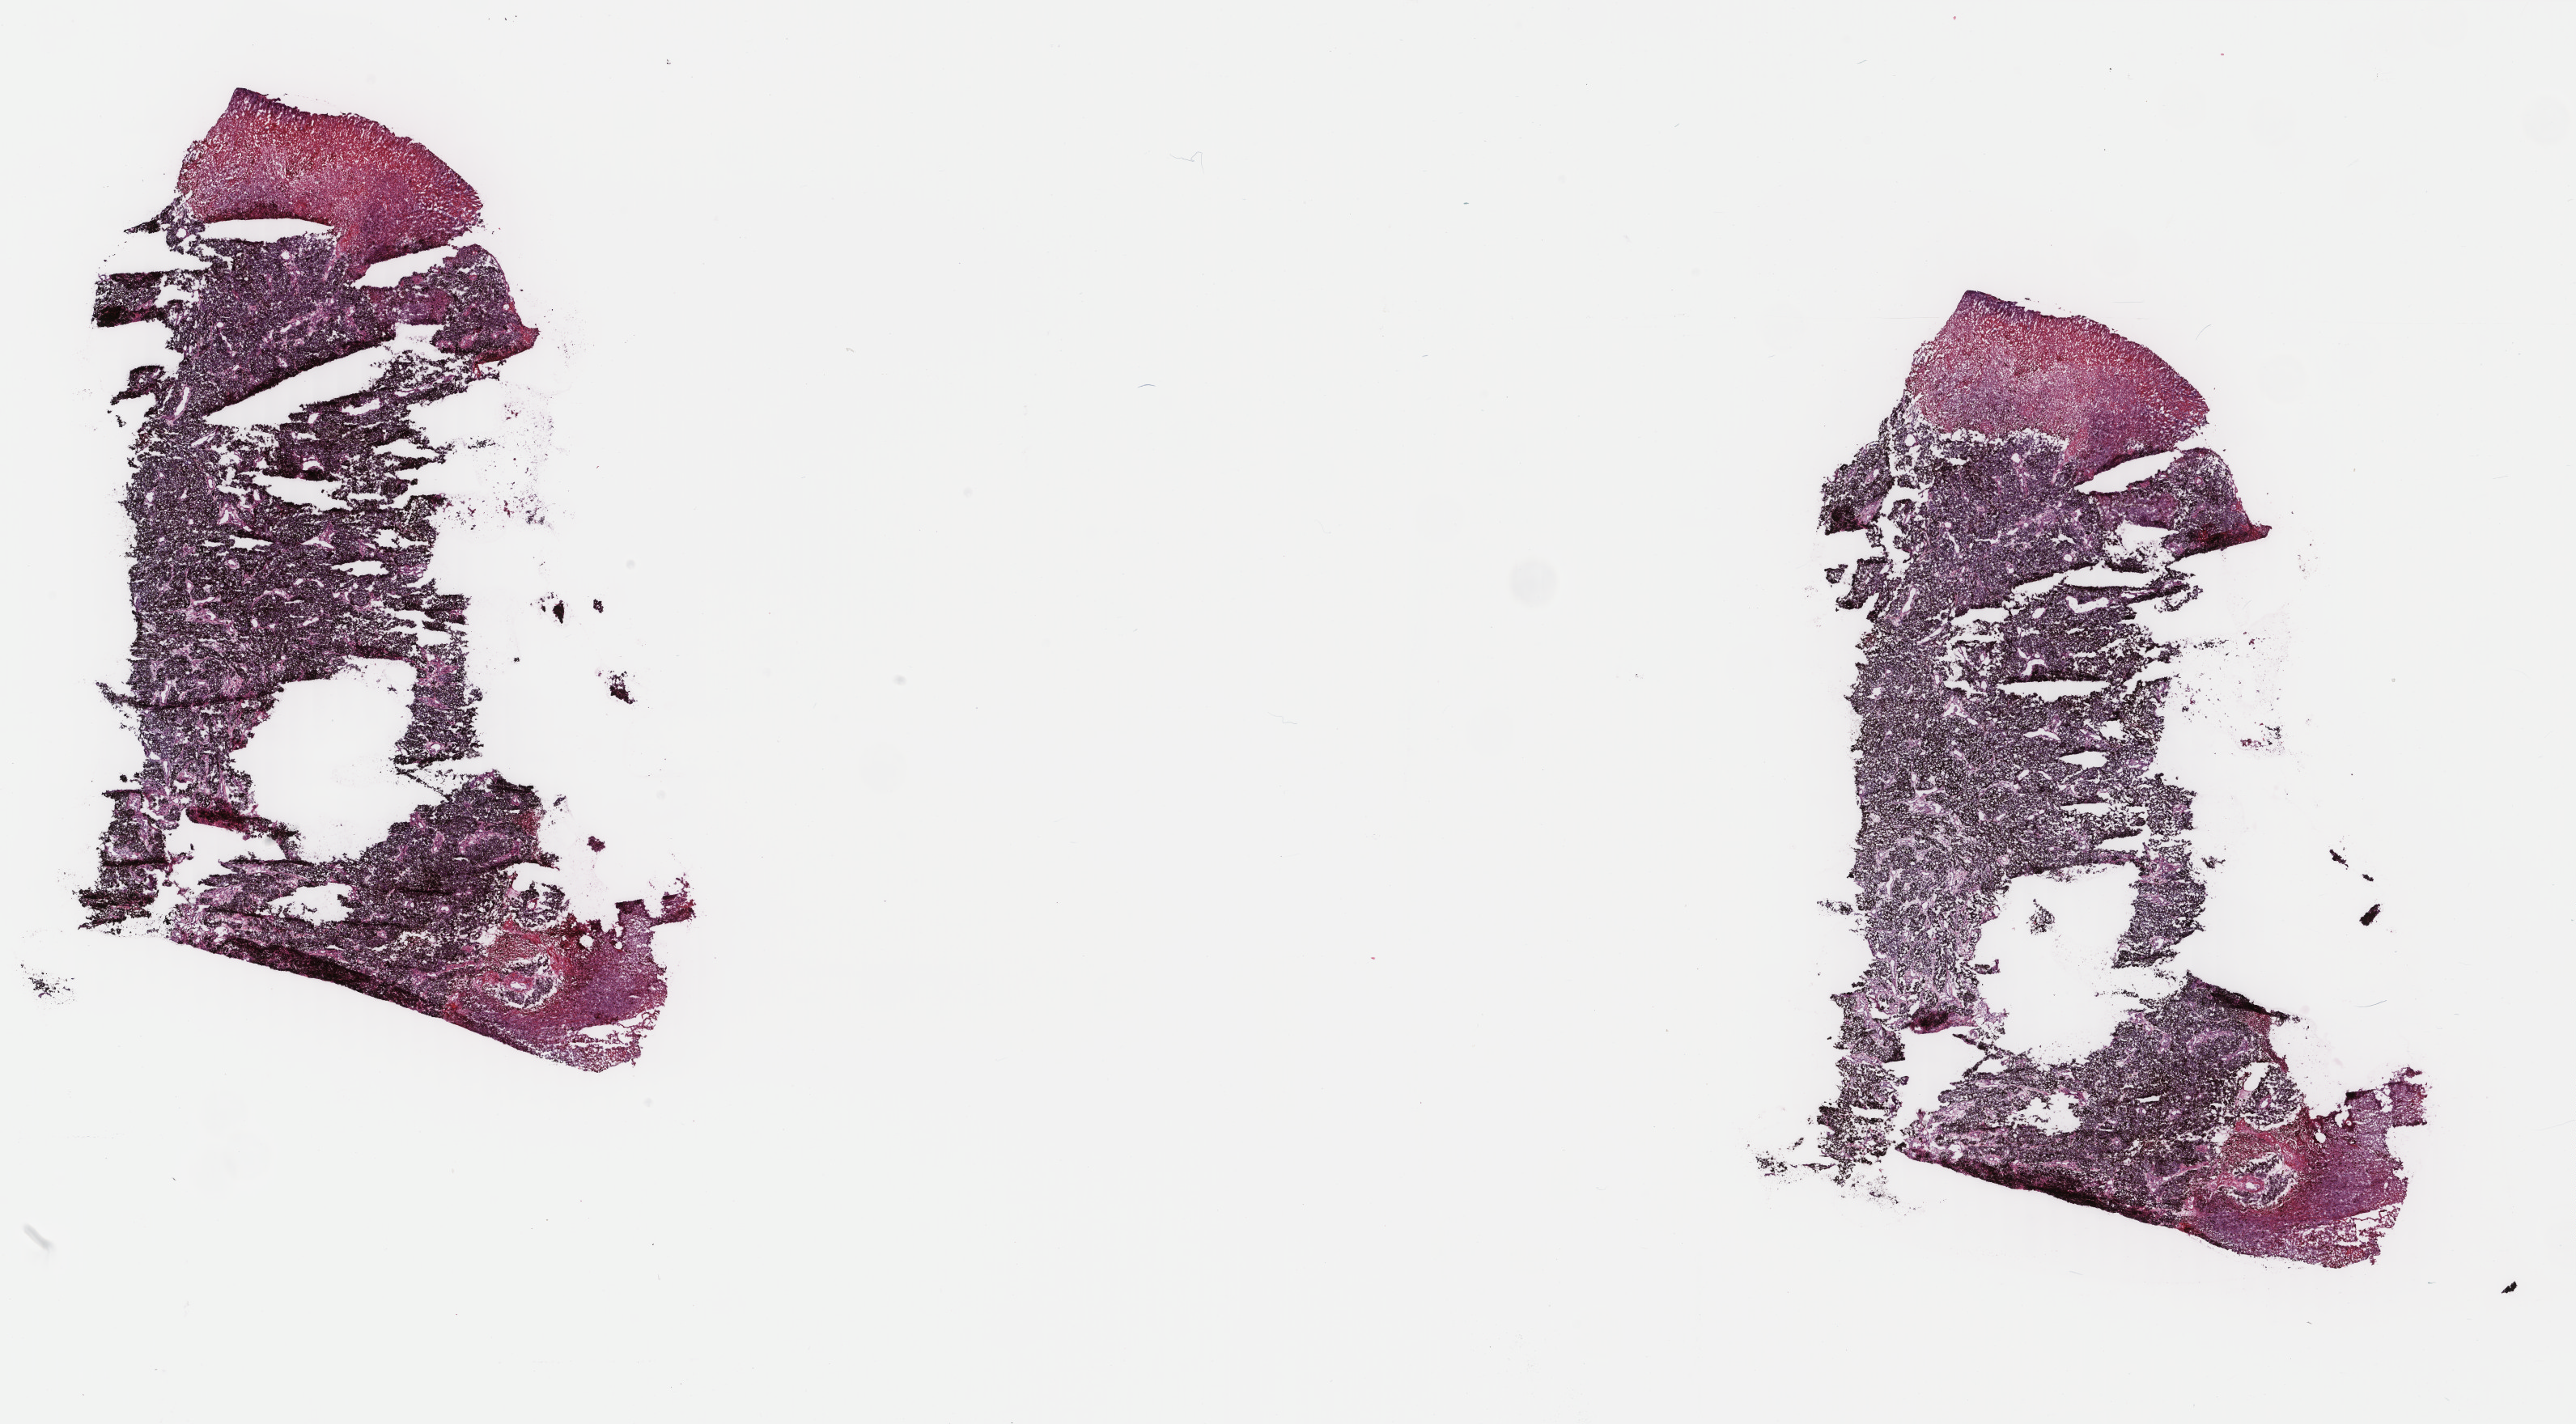
H&E-stained whole-slide image, shown as a low-resolution overview of the whole scanned area (about 25.3 x 14.0 mm, acquisition: 40x scan), frozen section from the top of the tissue portion, primary tumour sample from the skin. Female patient; age at initial diagnosis 84 years. Pathologist review of this section (percent, as recorded): tumour cells 90%, tumour nuclei 95%.
Diagnosis: Malignant melanoma, NOS.